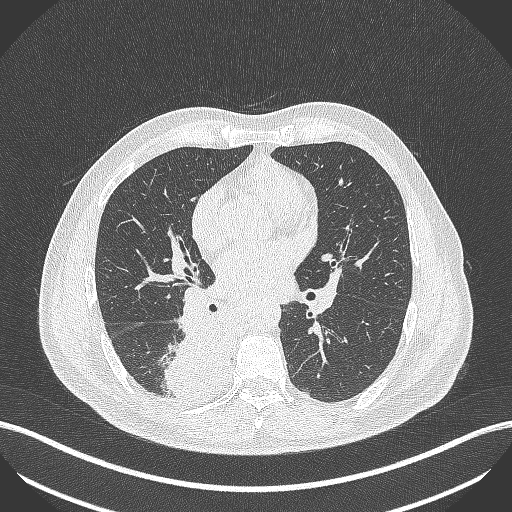
Chest CT, one axial slice; reconstruction kernel B70f; 100 kVp; lung window (W 1500 / L -600 HU); 1 mm slice thickness; 512 × 512 image matrix, field of view 400 × 400 mm. Patient: male, 61 years. Case-level facts recorded for this patient, not image findings: clinical TNM (as recorded): T1 N0 M0; histopathological grade: G3.
Structures marked on this image (bounding box drawn by a radiologist):
- lung tumour (recorded histology: small cell carcinoma): bounding box <165,315,240,407> (left, top, right, bottom; pixels)